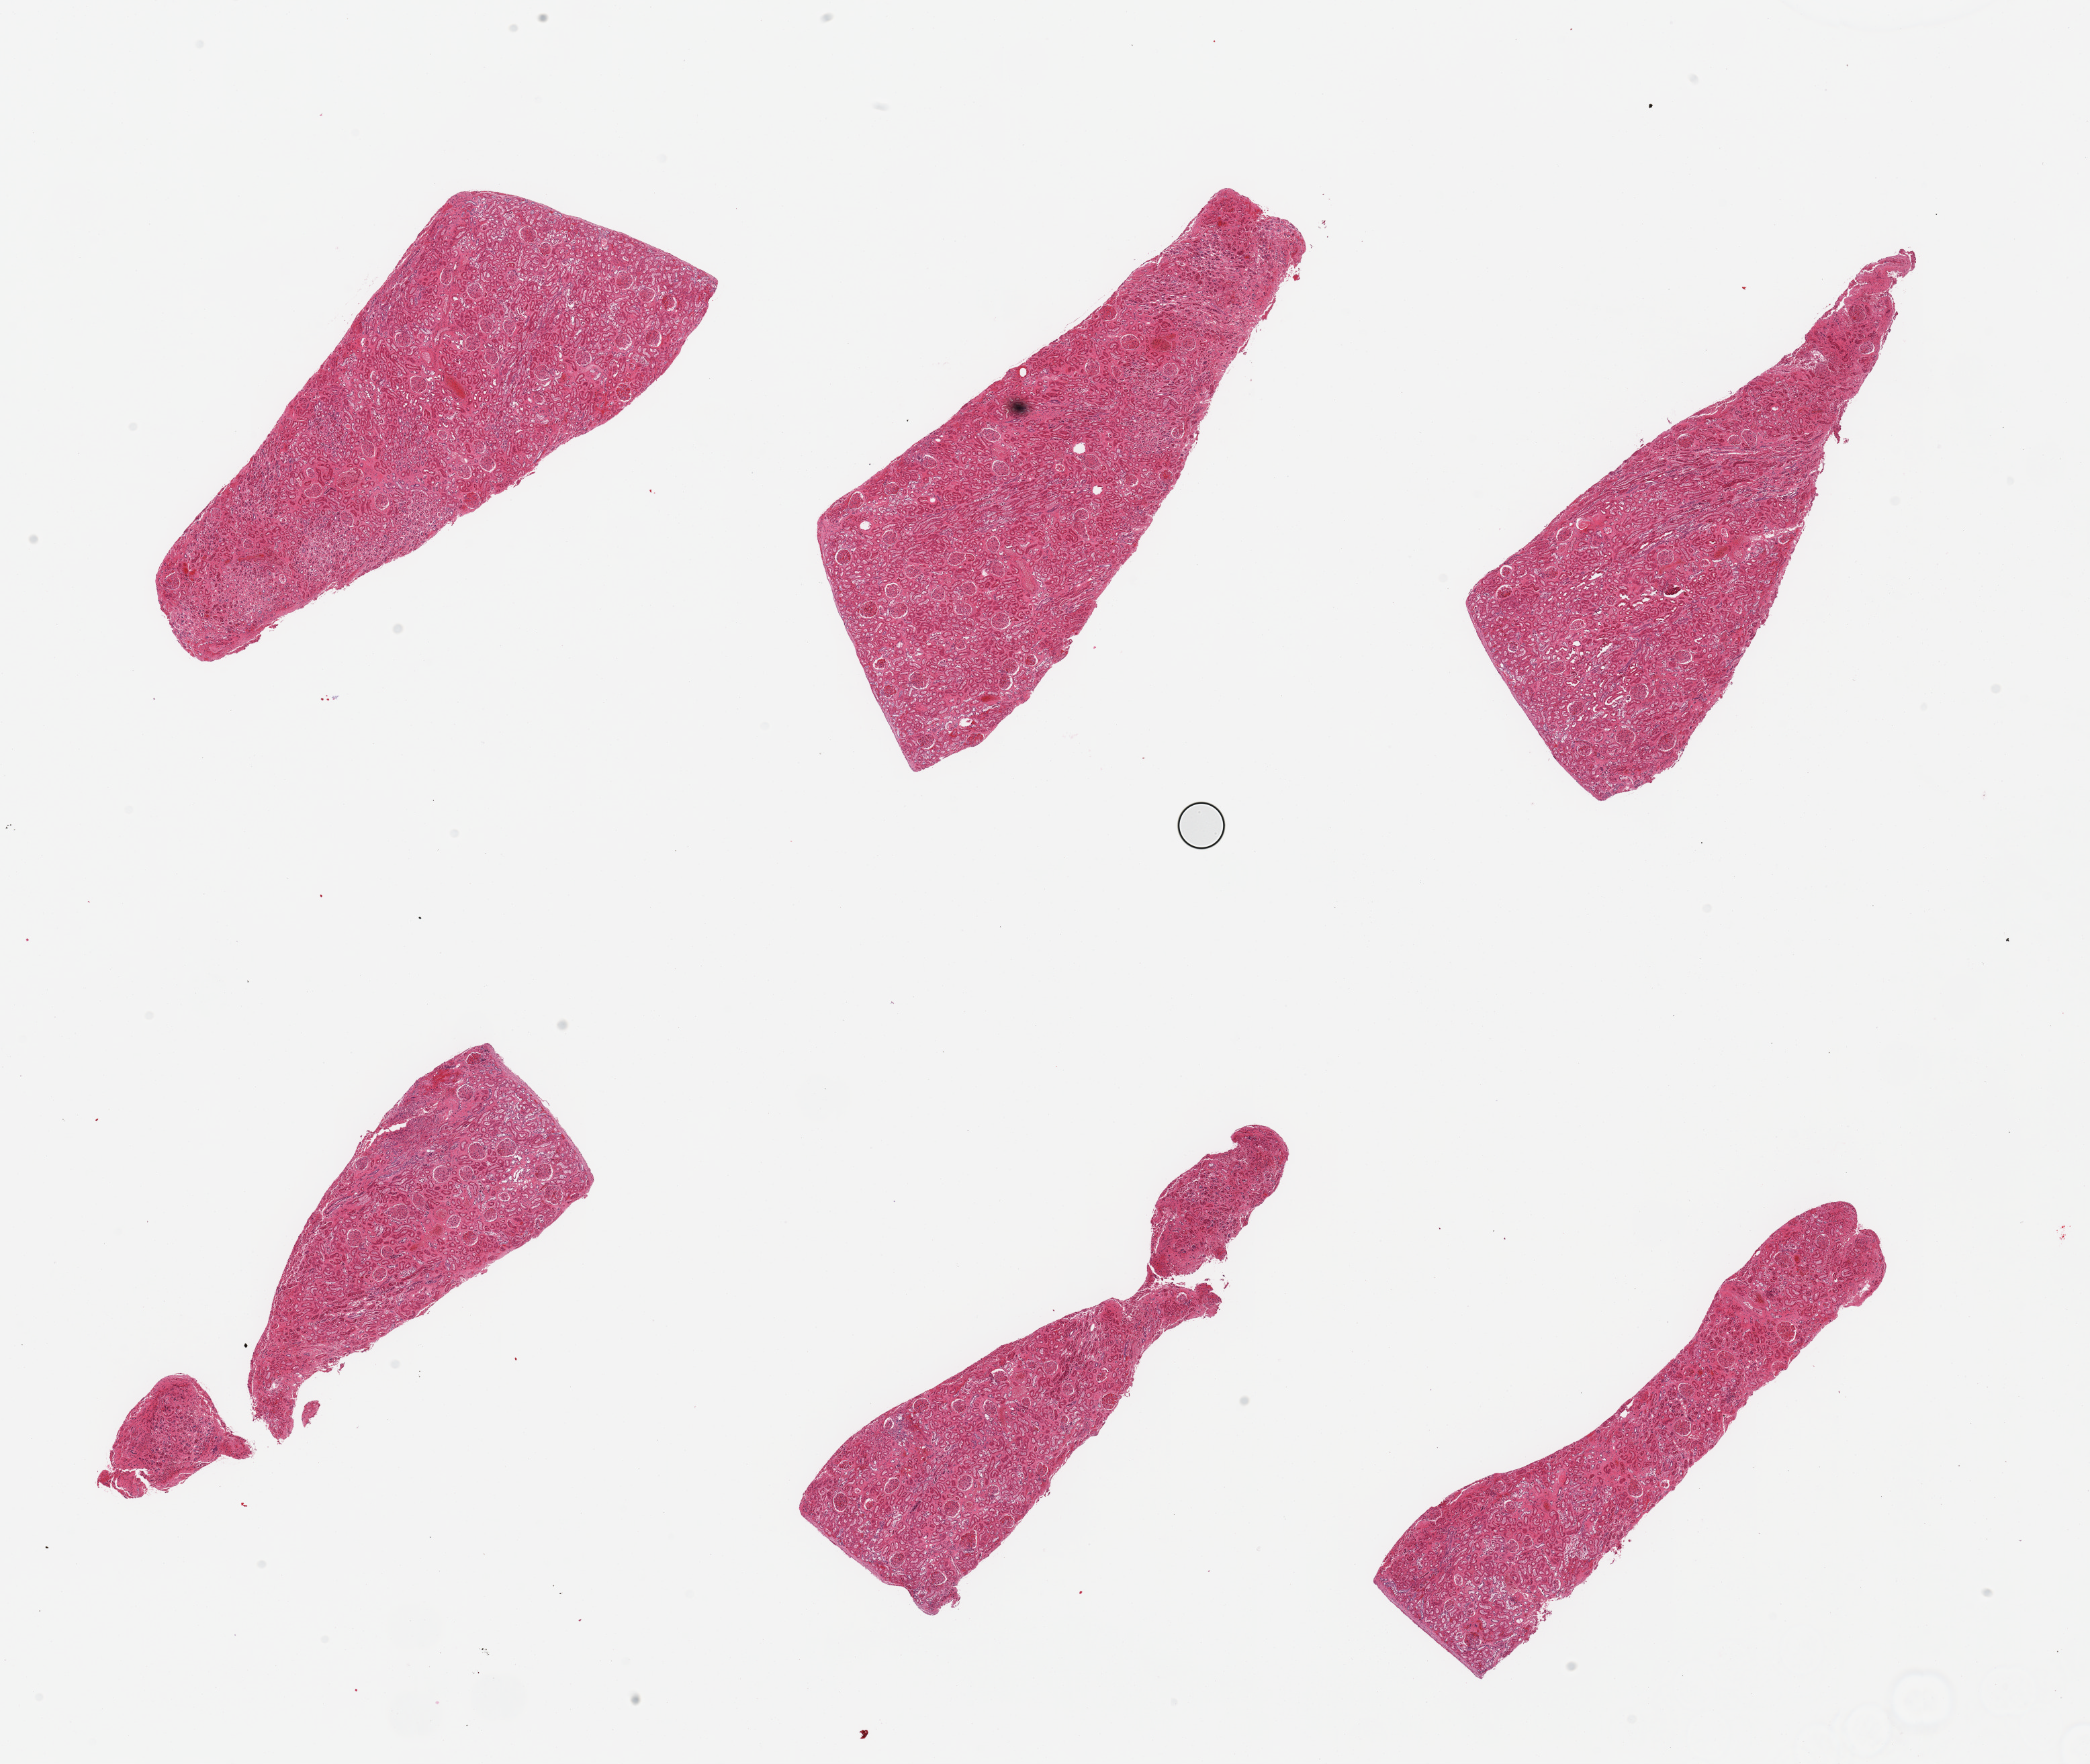
Digitized haematoxylin and eosin-stained section, low-resolution overview of the scanned area, about 24.6 x 20.8 mm (from a 20x scan). PAXgene-fixed paraffin-embedded (PFPE) section. Section of renal cortex (target tissue). Tissue donor sample. Donor: male.
Pathologist's review note for this sample: 6 pieces; mildly congested renal cortex, fibrosis.